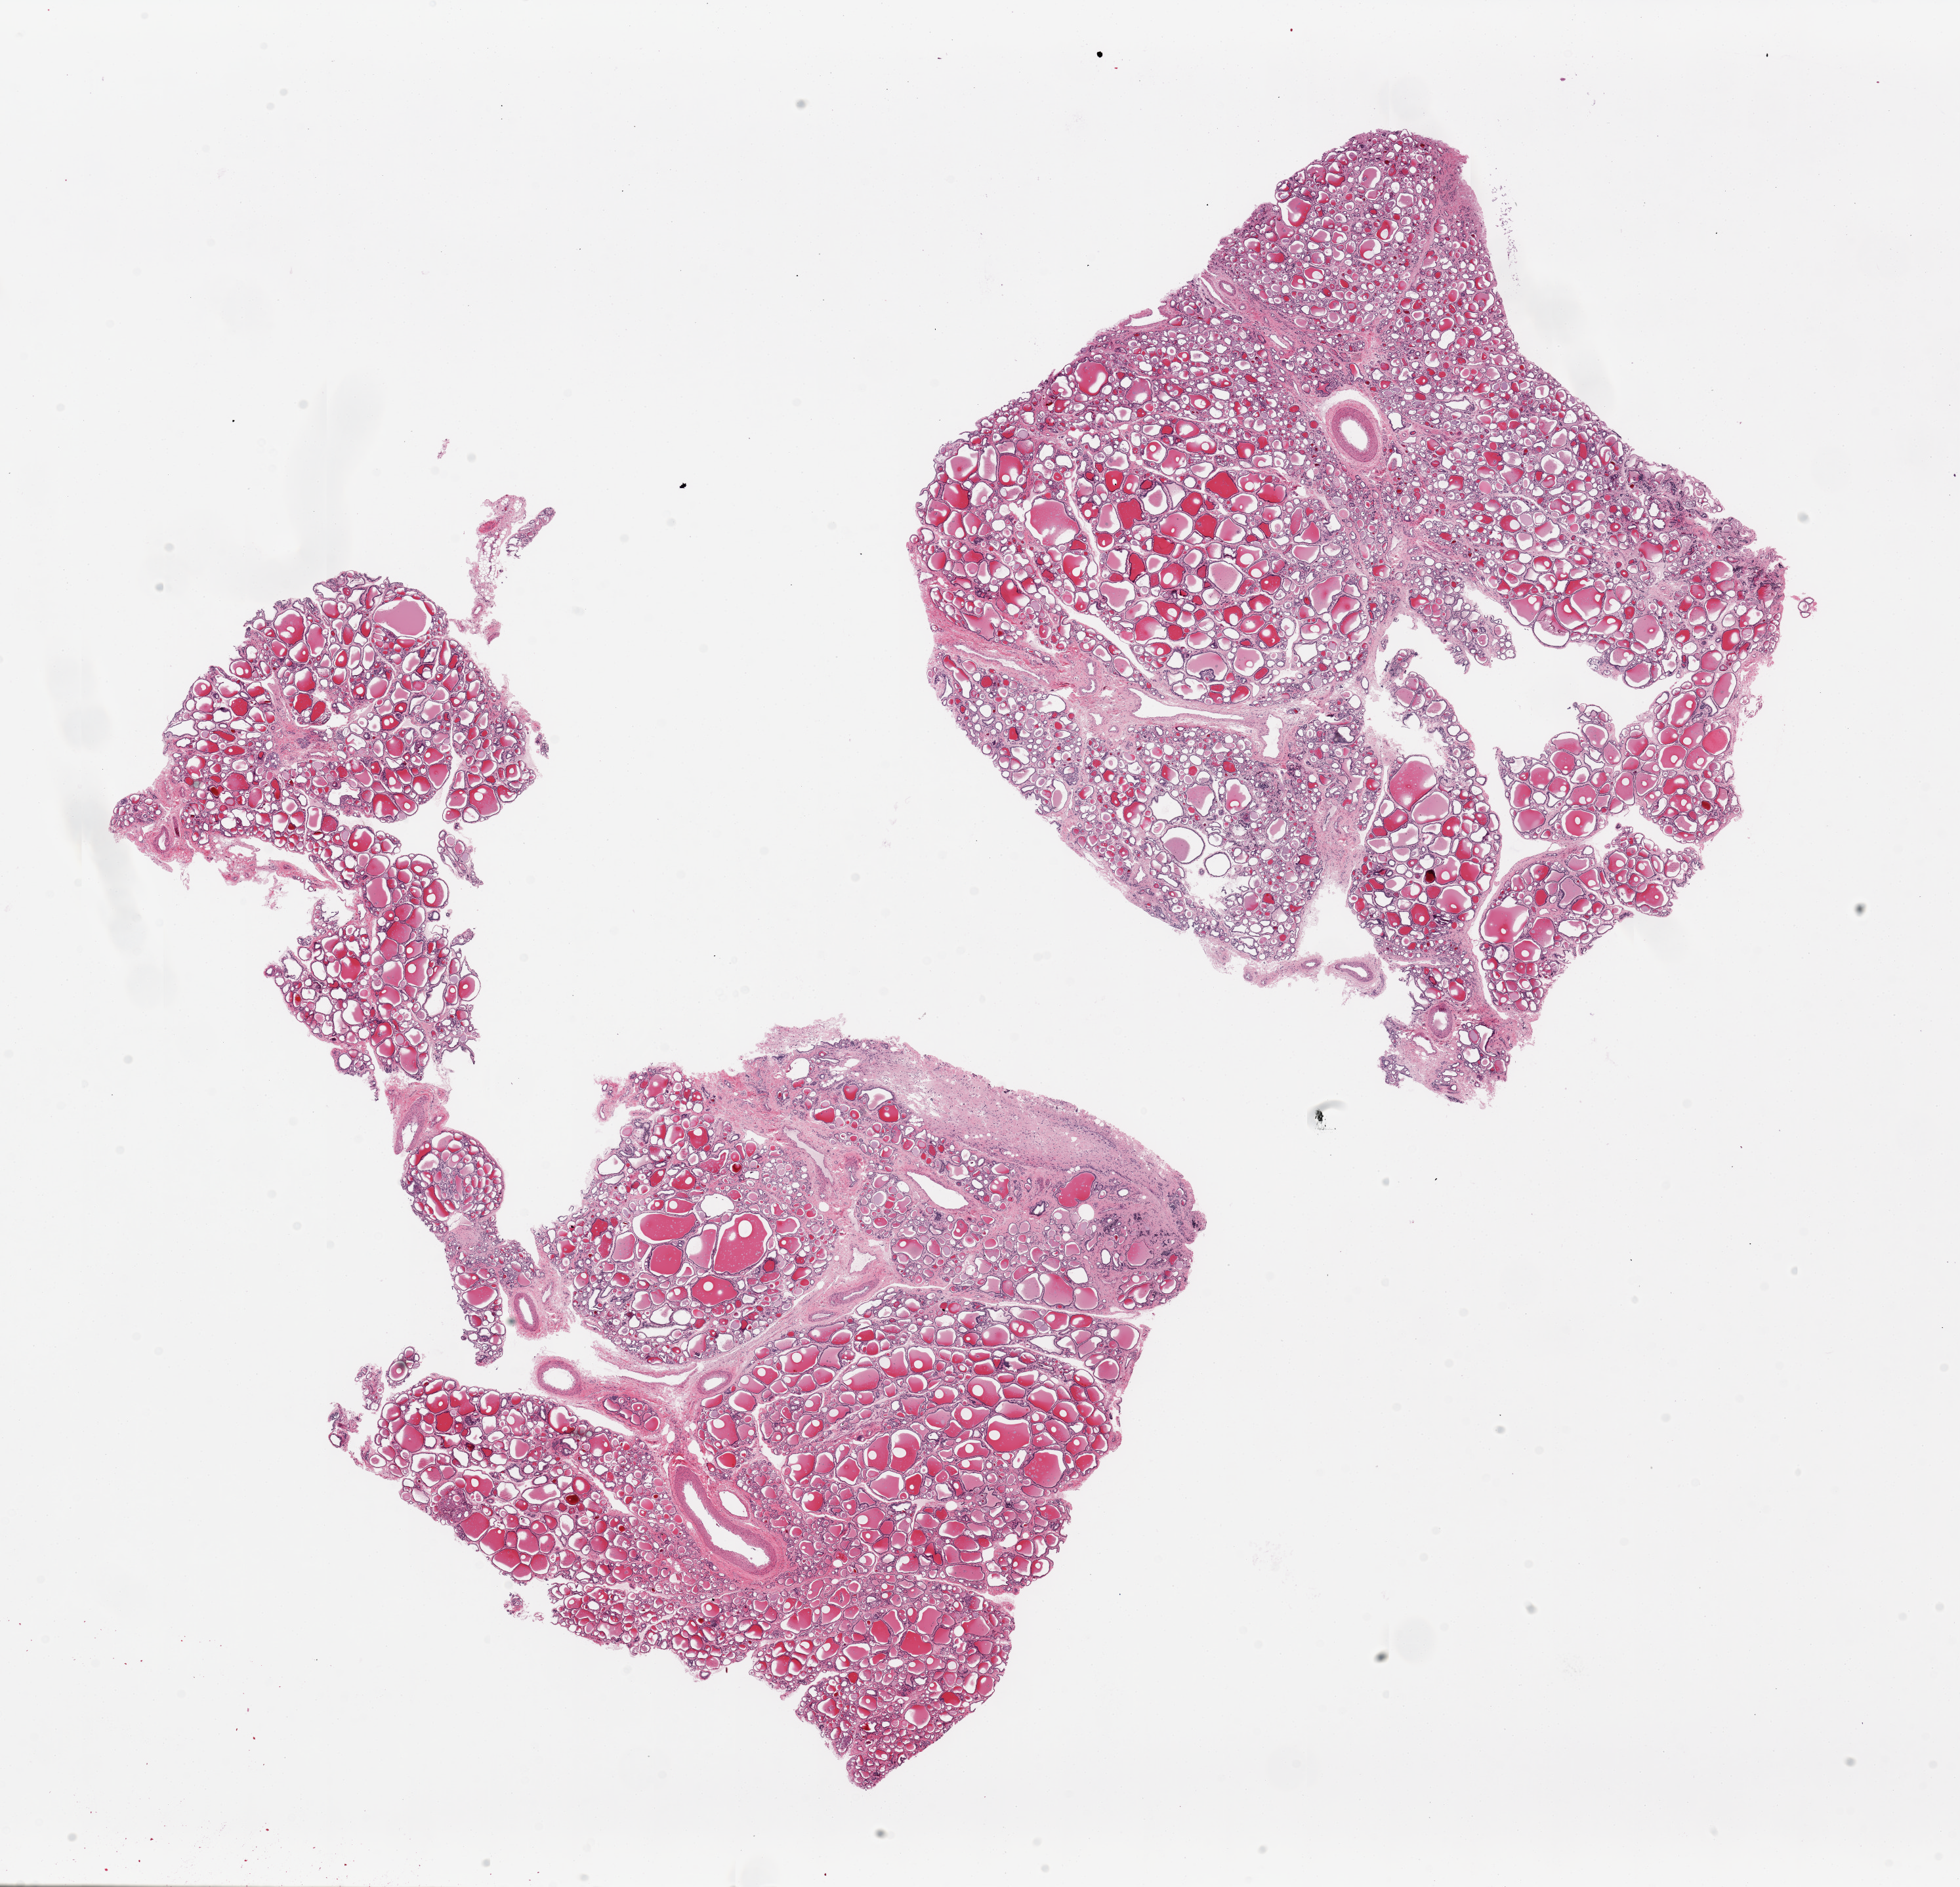
Digitized haematoxylin and eosin-stained section — whole scanned area (about 23.6 x 22.7 mm, slide scanned at 20x) shown as a low-resolution overview; PAXgene-fixed, paraffin-embedded tissue; target tissue: thyroid; donor tissue sample.
Reviewer comment on this tissue sample: 2 pieces, 15x9 & 10x9mm. Multinodular goitre with regressive changes (fibrous bands).